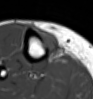
MRI of an extremity soft-tissue mass, one axial slice. Slice 17 of 54 in the series (ordered by position). MR volume resampled by the dataset authors to the PET/CT grid (not the native acquisition matrix). 3.27 mm slice thickness. 93 × 99 image matrix. Female patient. From the clinical record (not read from this slice): histological type: undifferentiated – high grade; grade: high; site of the primary tumour: right thigh.
Outlined on this slice (expert contour drawn on MRI and transferred to this co-registered scan by the dataset authors):
- gross tumour volume (mass): box from (x=36, y=29) to (x=60, y=58) px